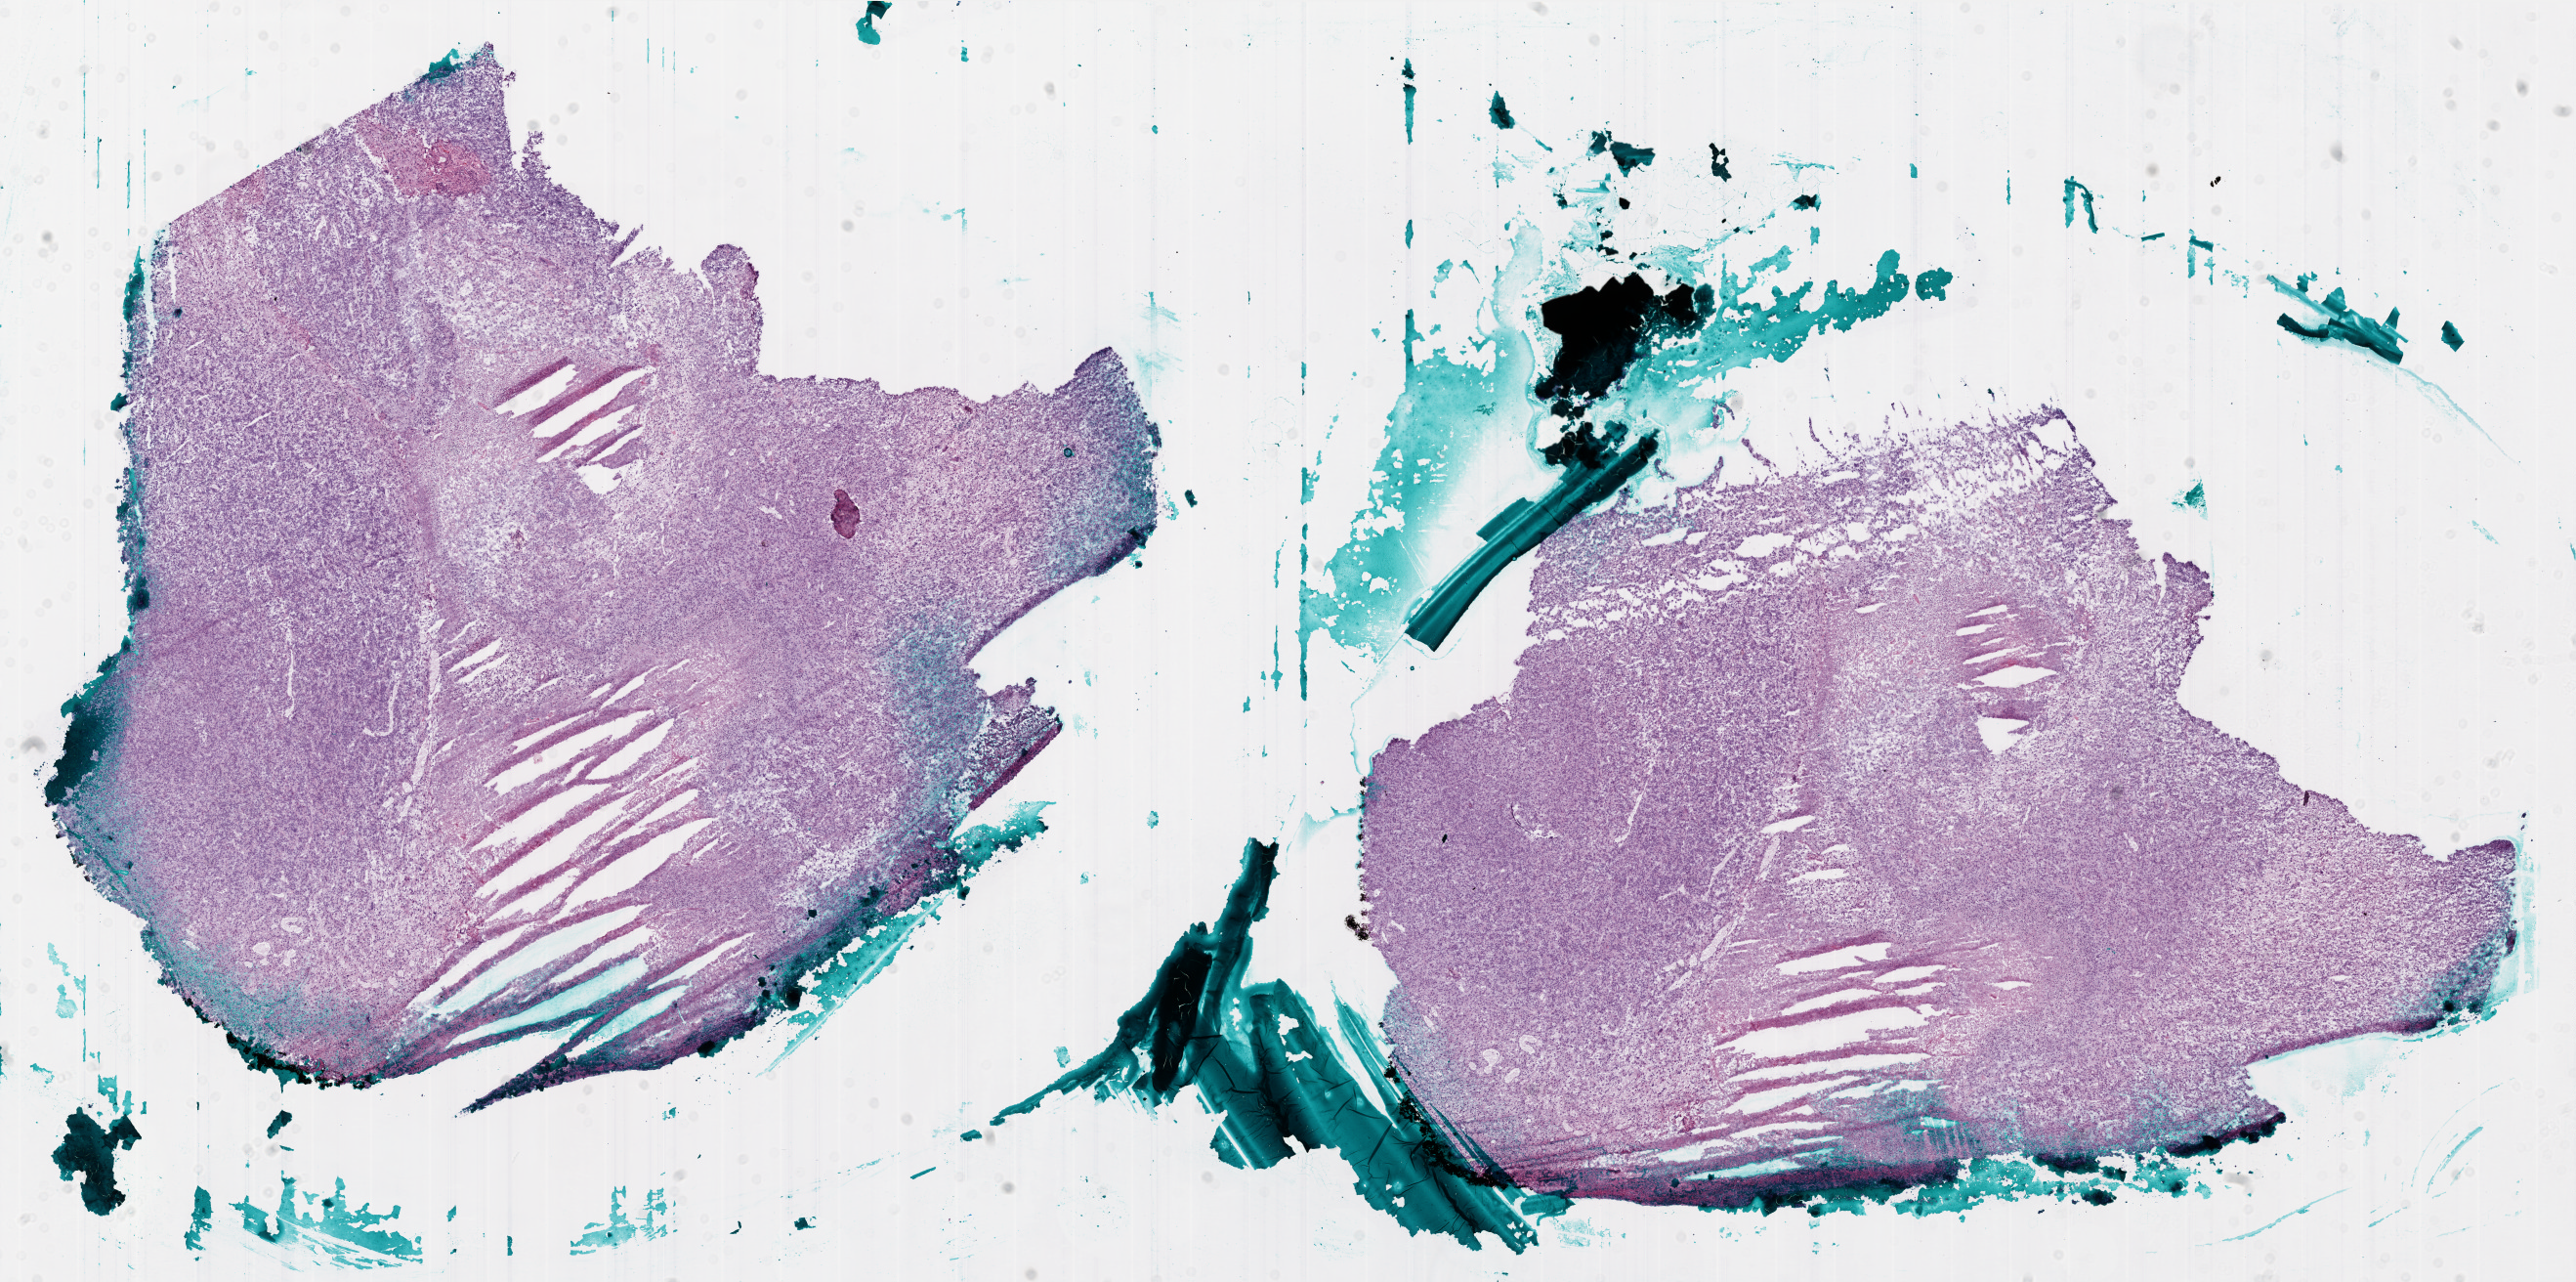
H&E-stained whole-slide image — whole scanned area (about 21.2 x 10.6 mm, acquisition: 20x scan) shown as a low-resolution overview, frozen section, sample: primary tumour, brain. Male patient; age at initial diagnosis 68 years. Slide review estimates, as recorded: tumour cells 68%, tumour nuclei 95%, normal cells 0%, stromal cells 0%, necrosis 32%.
• histologic diagnosis: Glioblastoma